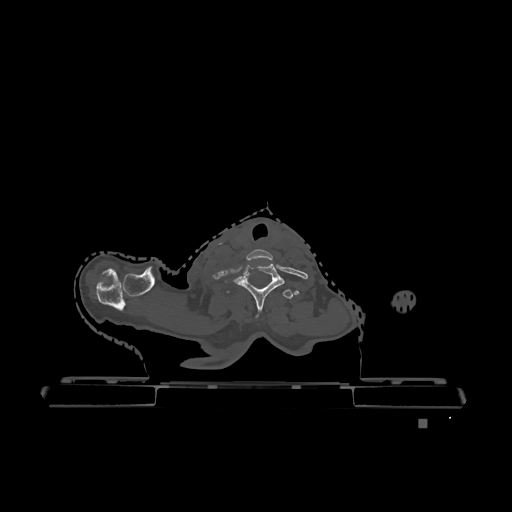
CT including the spine, one axial slice; position 1026 of 1317 along the scan axis; bone window (W 1800 / L 400 HU); 0.5 mm slice thickness; 512 × 512 image matrix. Patient: female, 74 years. From the clinical record (not read from this slice): primary cancer: lung; vertebrae with lytic lesions (as recorded): T1, T4, T5, T6, L4, L5.
Annotated regions visible in this slice (semi-automatically segmented with operator editing):
- T1 vertebra: box from (x=227, y=289) to (x=293, y=299) px